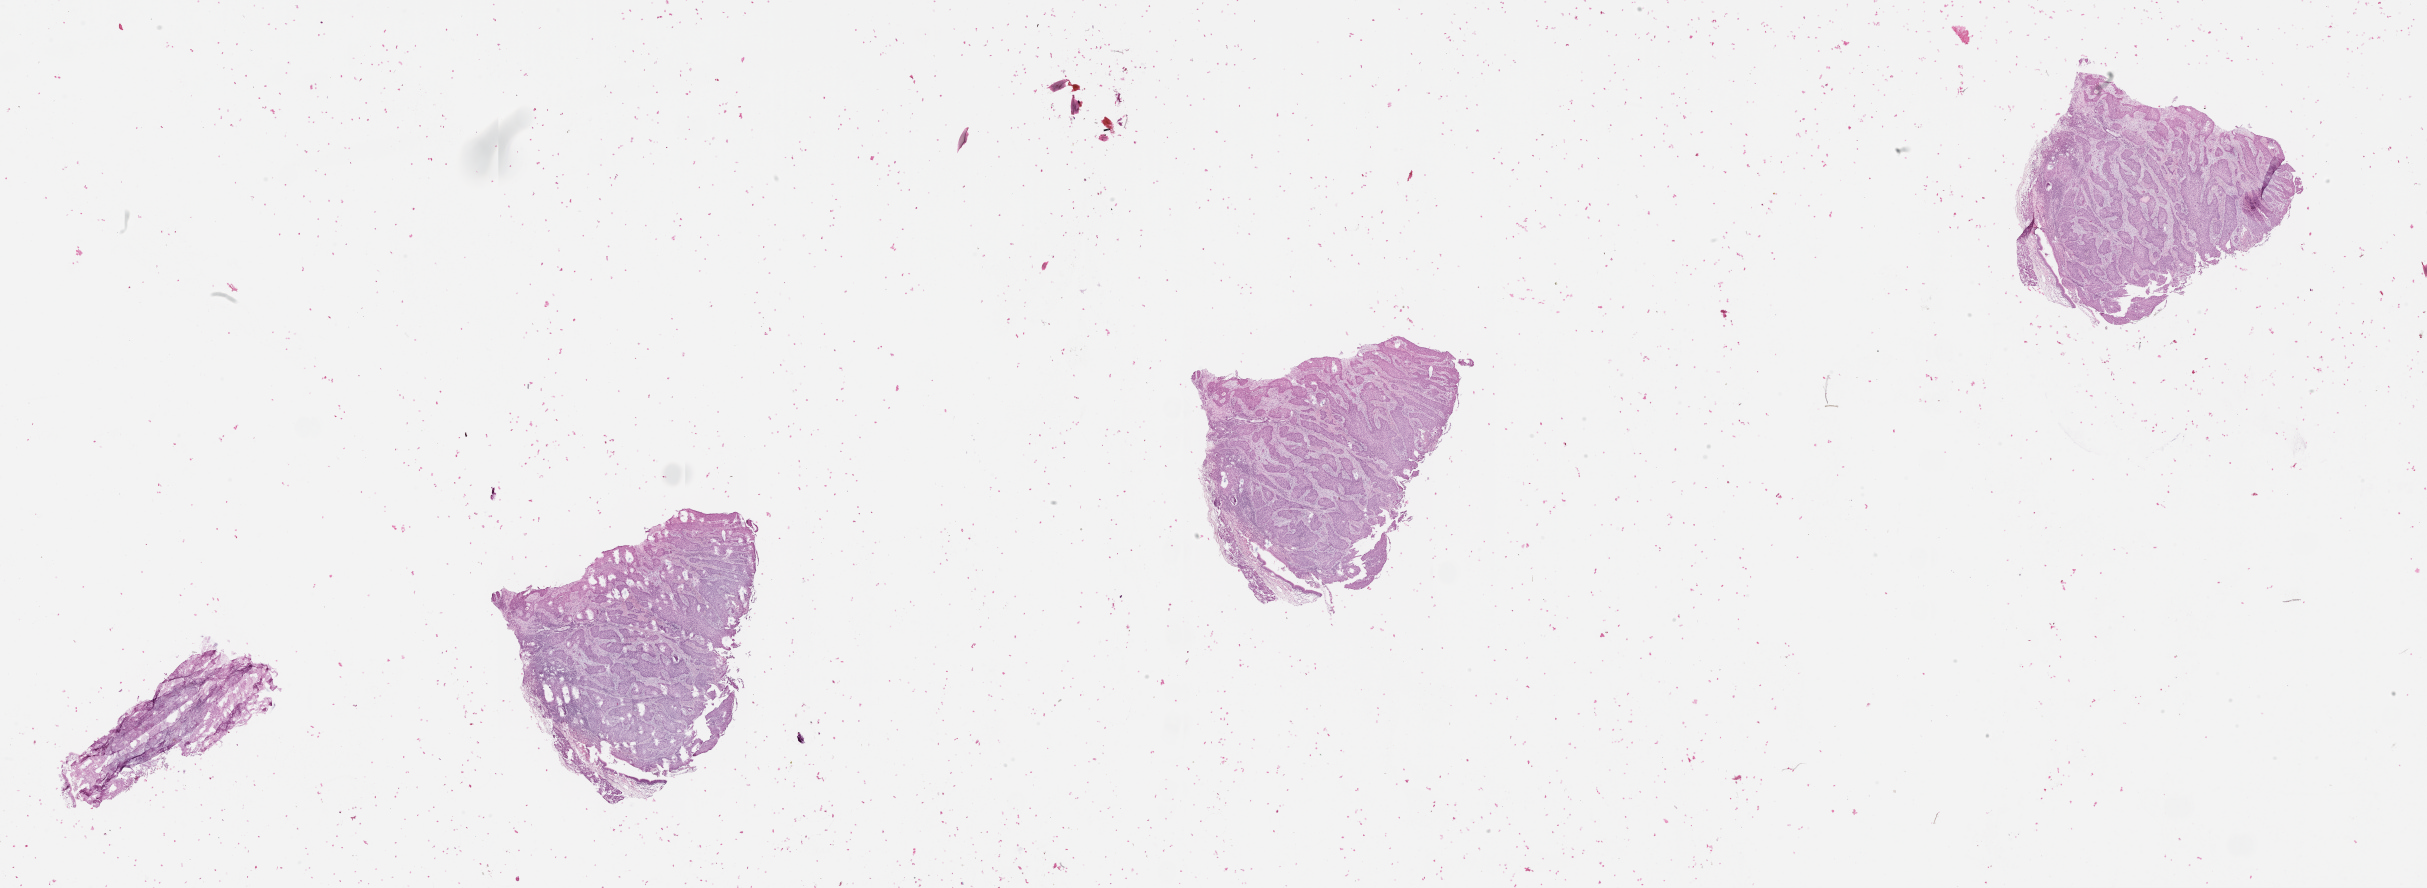
Whole-slide histology image, H&E-stained — whole scanned area (about 39.1 x 14.3 mm) shown as a low-resolution overview, tumour tissue sample, lung. Female, 61 y/o.
* patient diagnosis (cohort enrolment): squamous cell carcinoma (lung)